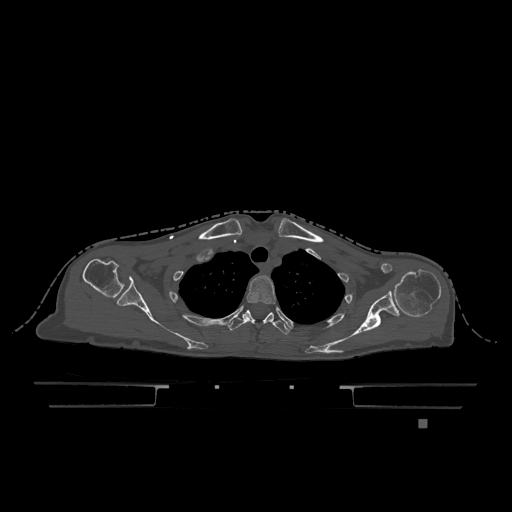
CT including the spine, one axial slice; bone window (W 1800 / L 400 HU); 0.5 mm slice thickness; 512 × 512 image matrix. Patient: female, 74 years. Case-level facts recorded for this patient, not image findings: primary cancer: lung.
Annotated regions visible in this slice (semi-automatically segmented with operator editing):
- T2 vertebra: bounding box [x1, y1, x2, y2] px = [246, 276, 276, 304]
- T3 vertebra: [228, 310, 290, 335]
- T6 vertebra: [268, 312, 274, 317]